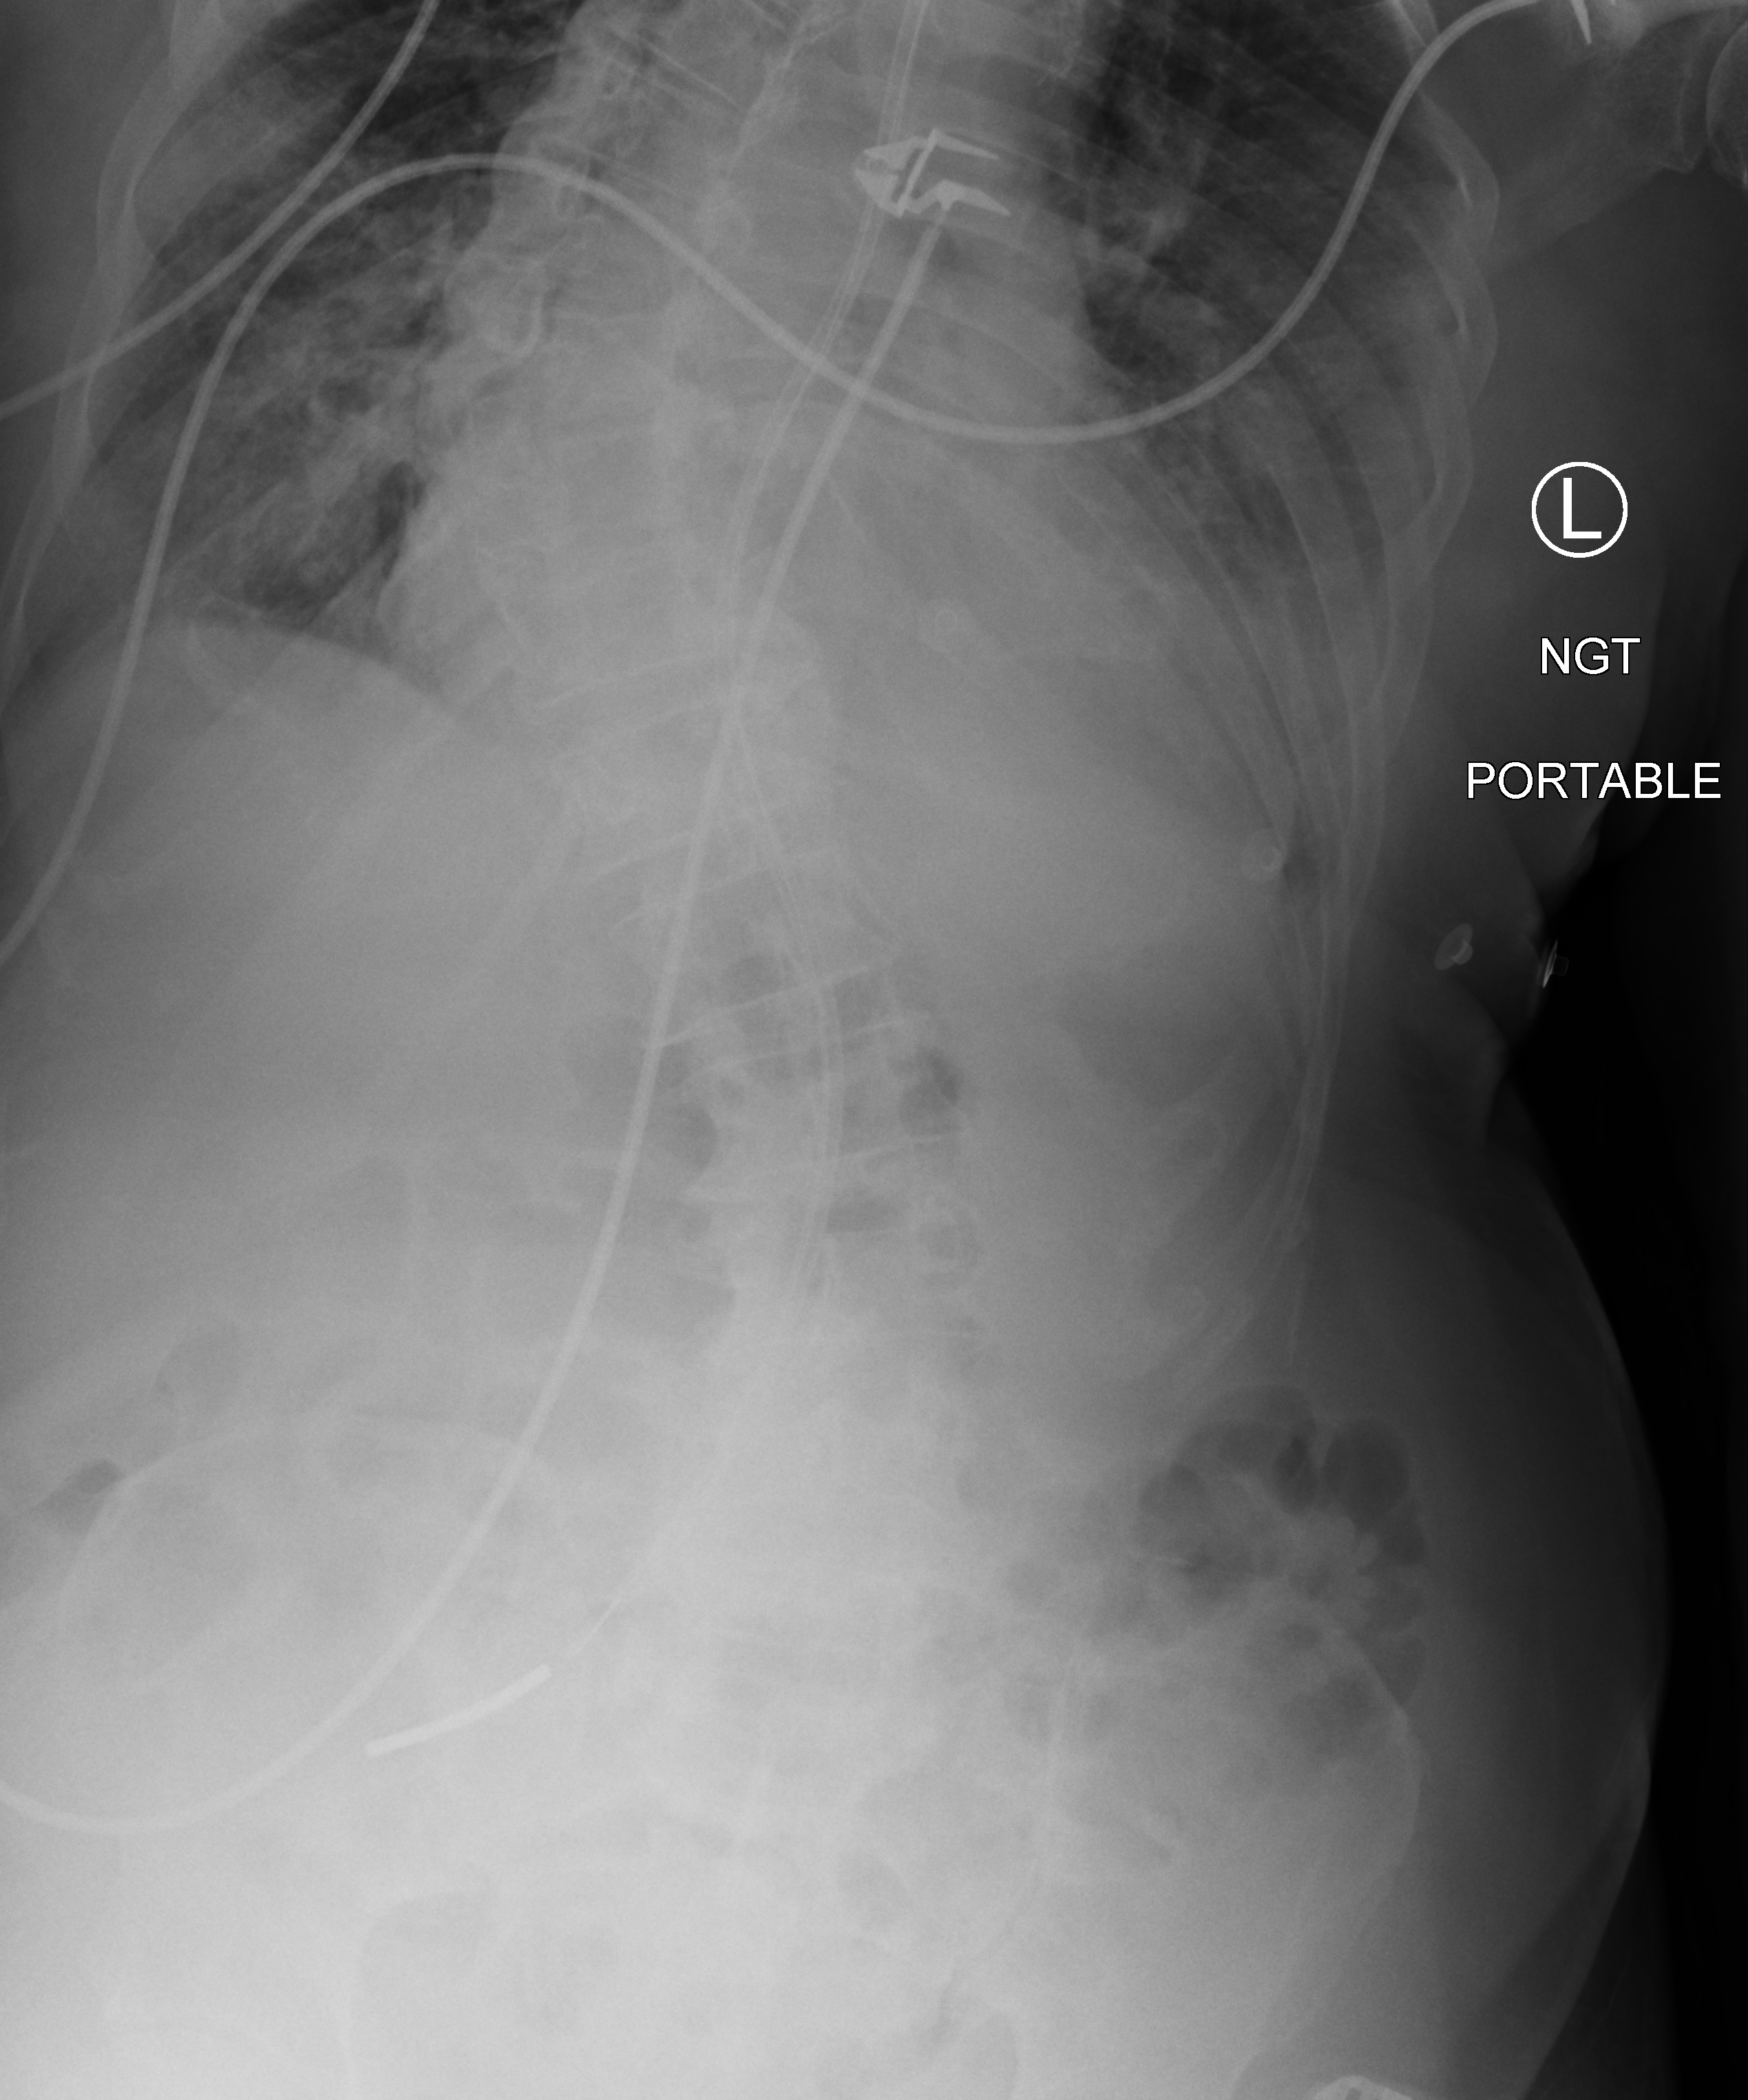
Bedside chest radiograph (computed radiography). Male patient hospitalised with COVID-19, age 75–90 years.
From the hospital-stay record, not from the radiograph (when in the stay this image was taken is not recorded): mechanically ventilated during this hospital stay: no; length of hospital stay: 12 days.